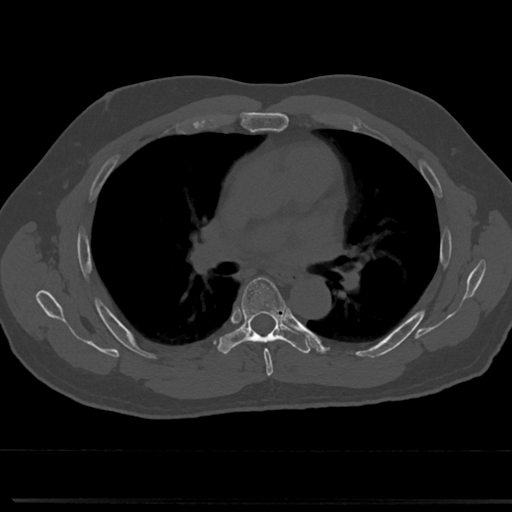
CT including the spine, one axial slice; slice 464 of 817 in the series (ordered by position); reconstruction kernel Br40s/3; 120 kVp; bone window (W 1800 / L 400 HU); 0.5 mm slice thickness; 512 × 512 image matrix. Male patient, age 61 years. Case-level facts recorded for this patient, not image findings: primary cancer: prostate.
Structures marked on this image (semi-automatic segmentation, software-assisted and operator-edited):
- T5 vertebra: bounding box [x1, y1, x2, y2] px = [243, 332, 282, 365]
- T6 vertebra: [217, 275, 308, 355]